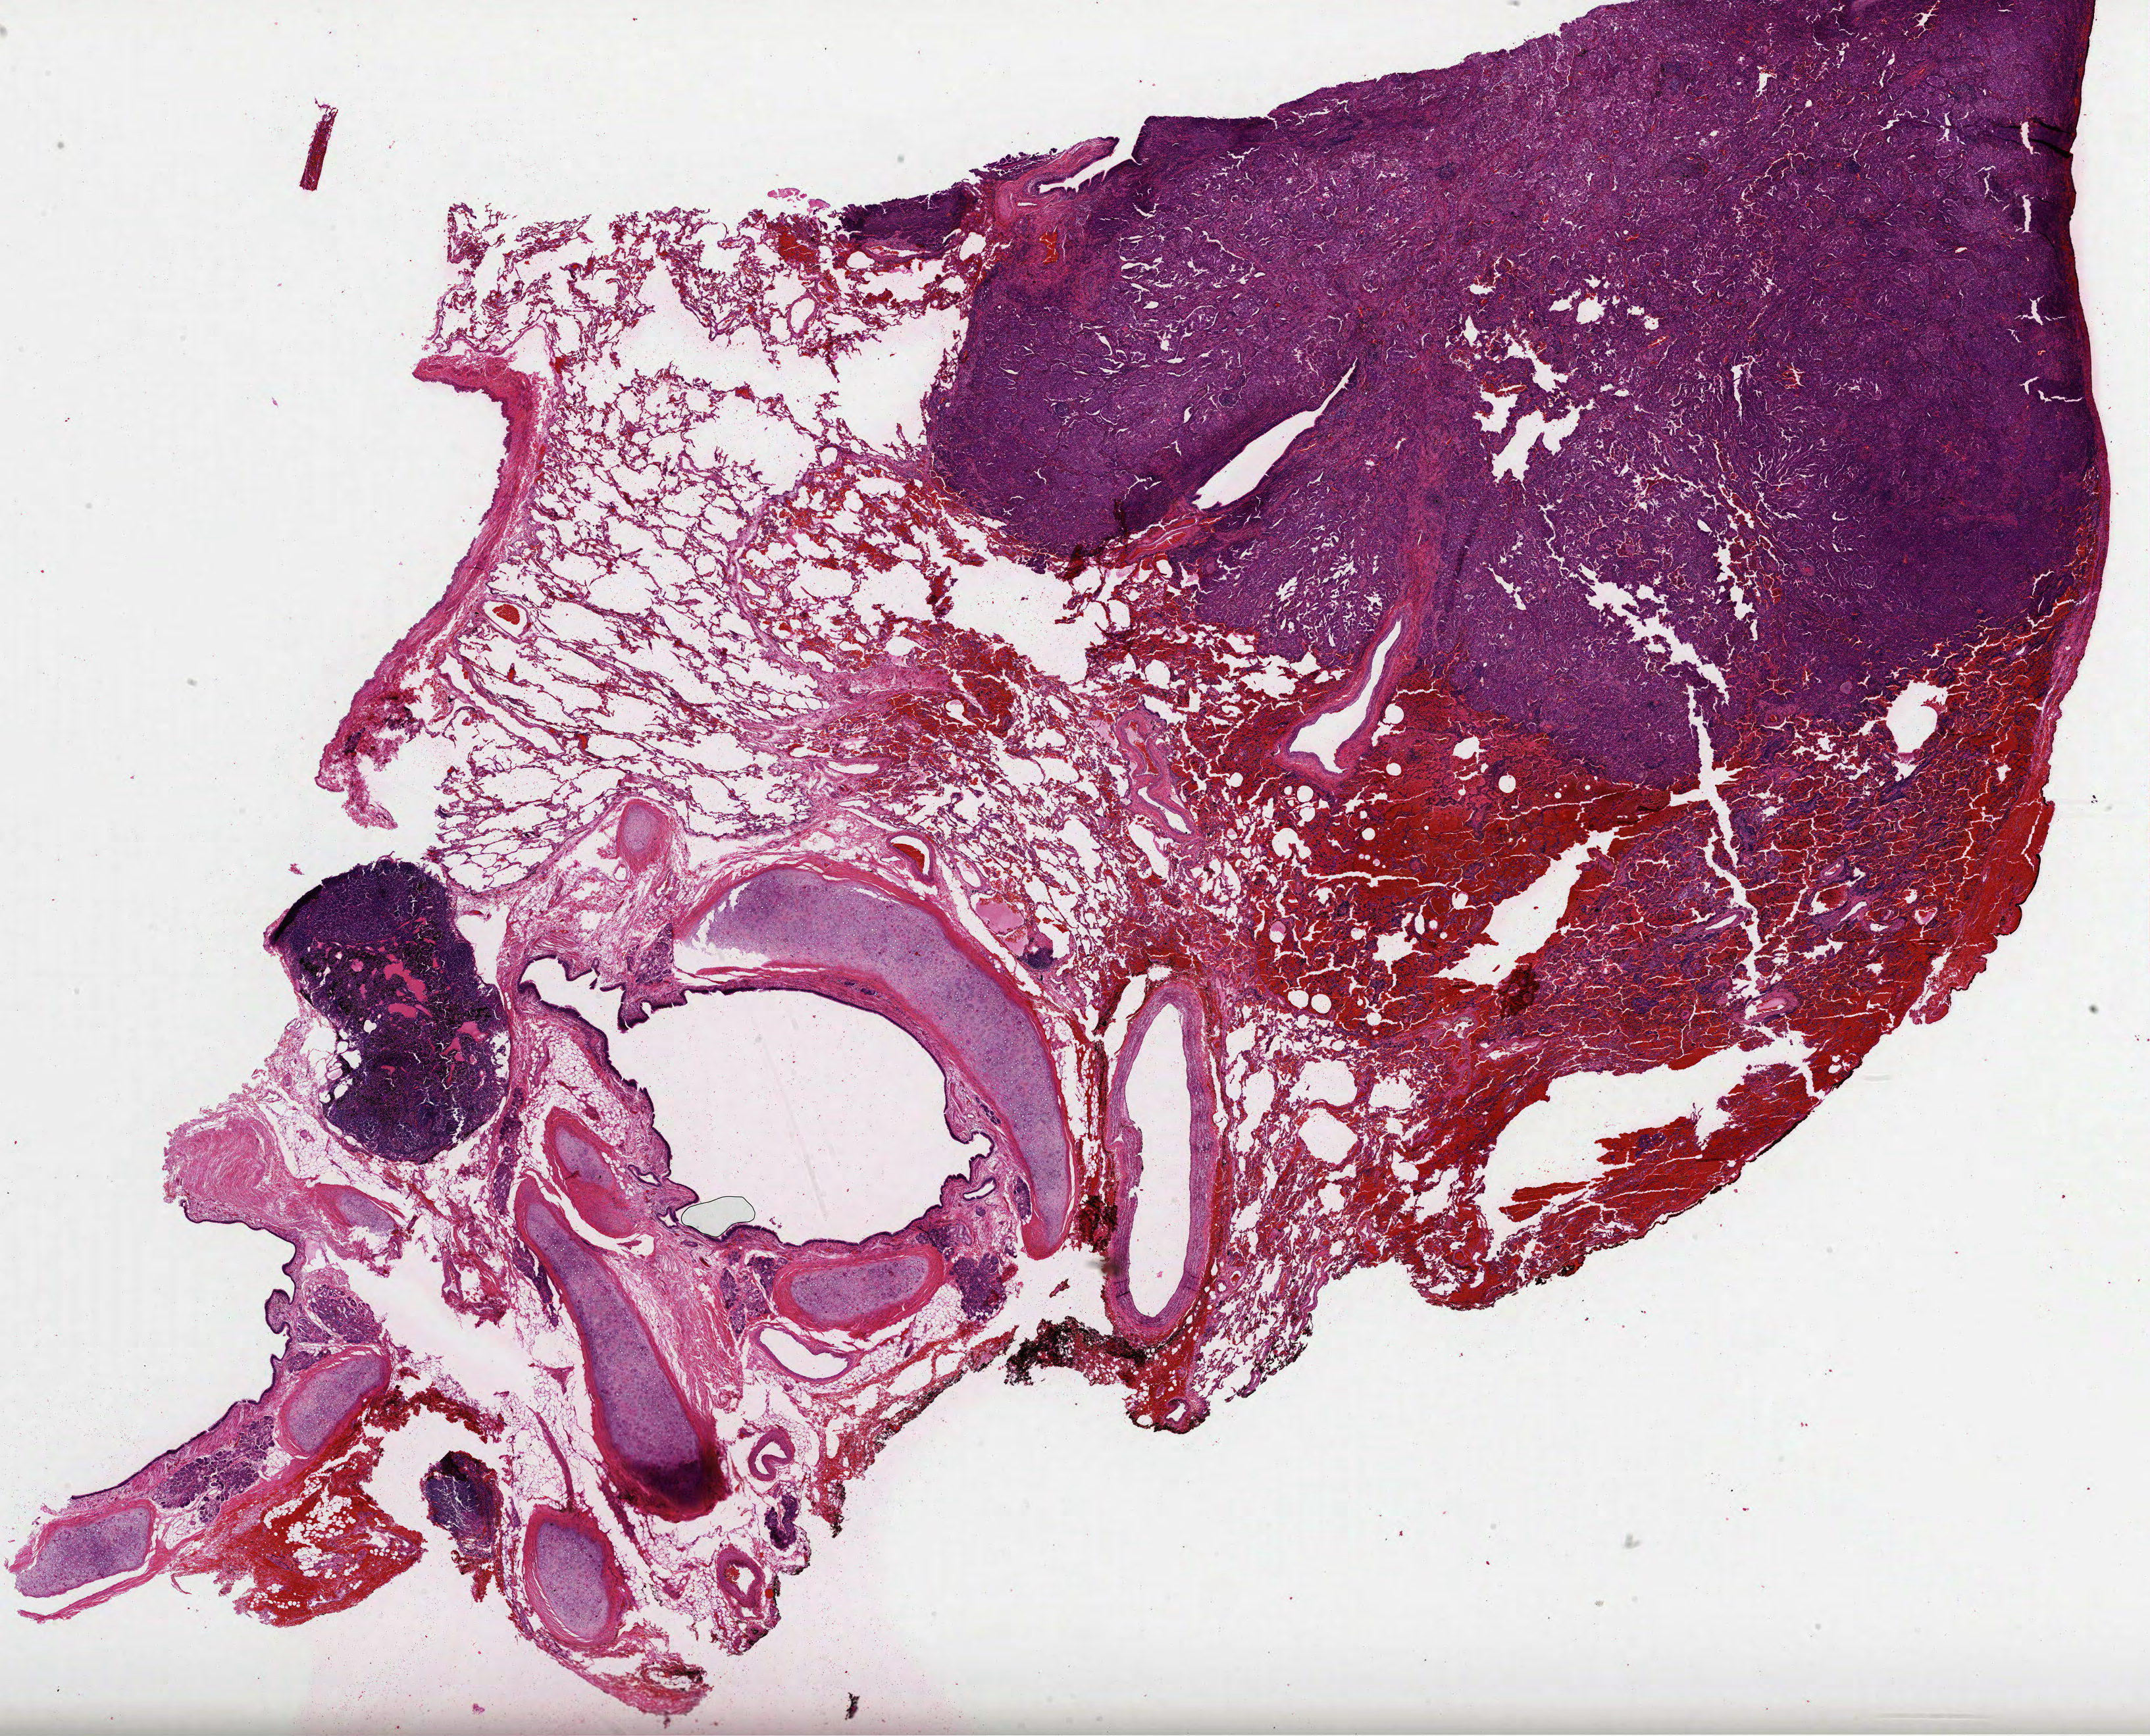
Whole-slide histology image, H&E, shown as a low-resolution overview of the whole scanned area (about 26.3 x 21.3 mm). FFPE section. Primary tumour sample from the lung. Male, age 82 years at initial diagnosis.
Diagnosis: Papillary adenocarcinoma, NOS (upper lobe, lung). AJCC pathologic stage: IIIA (7th edition).